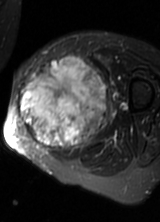
MRI of an extremity soft-tissue mass, one axial slice. Slice 31 of 69 in the series (ordered by position). T2-weighted fat-saturated. MR volume resampled by the dataset authors to the PET/CT grid (not the native acquisition matrix). 3.27 mm slice thickness. 160 × 222 image matrix. Female patient. Case-level facts recorded for this patient, not image findings: histological type: pleomorphic leiomyosarcoma; grade: high; site of the primary tumour: left thigh.
Structures marked on this image (expert contour drawn on MRI and transferred to this co-registered scan by the dataset authors):
- gross tumour volume including surrounding oedema: bounding box [x1, y1, x2, y2] px = [18, 57, 108, 153]
- gross tumour volume (mass): [18, 59, 108, 151]